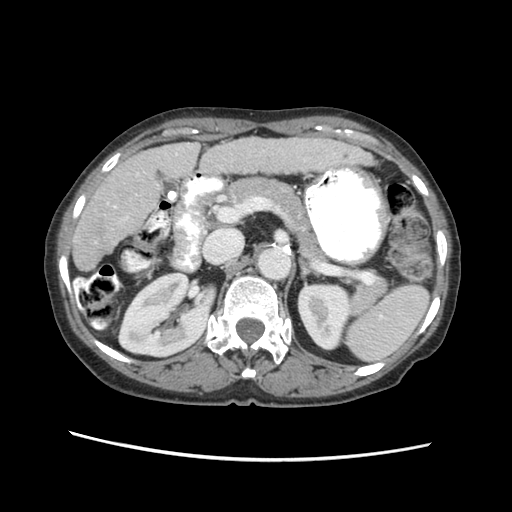
Contrast-enhanced abdominal CT (liver protocol), one axial slice; reconstruction kernel STANDARD; 120 kVp; soft-tissue window (W 400 / L 40 HU); 512 × 512 image matrix, field of view 340 × 340 mm. Case-level facts recorded for this patient, not image findings: diagnosis: hepatocellular carcinoma (patient treated with transarterial chemoembolisation; whether this scan precedes or follows treatment is not stated here); TNM stage (as recorded): Stage-I; Child-Pugh class: B; tumour differentiation: well differentiated.
Outlined on this slice (semi-automatically segmented with operator editing):
- liver parenchyma outside the tumour (the mass and vessels are separate outlines, so this box may not span the whole liver): box from (x=70, y=132) to (x=378, y=270) px
- liver vessels: (x=133, y=152)–(x=174, y=174)